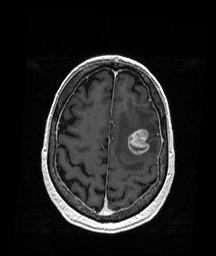
Brain MRI from a brain-tumour surgery series, one axial slice. Position 52 of 176 along the scan axis. T1-weighted post-contrast. 1 mm slice thickness. 216 × 256 image matrix, field of view 211 × 250 mm. Case-level facts recorded for this patient, not image findings: histopathology: Metastatic Melanoma; tumour location: Left Frontal.
Structures marked on this image (outlined manually by an expert reader):
- tumour: bounding box <127,128,149,156> (left, top, right, bottom; pixels)